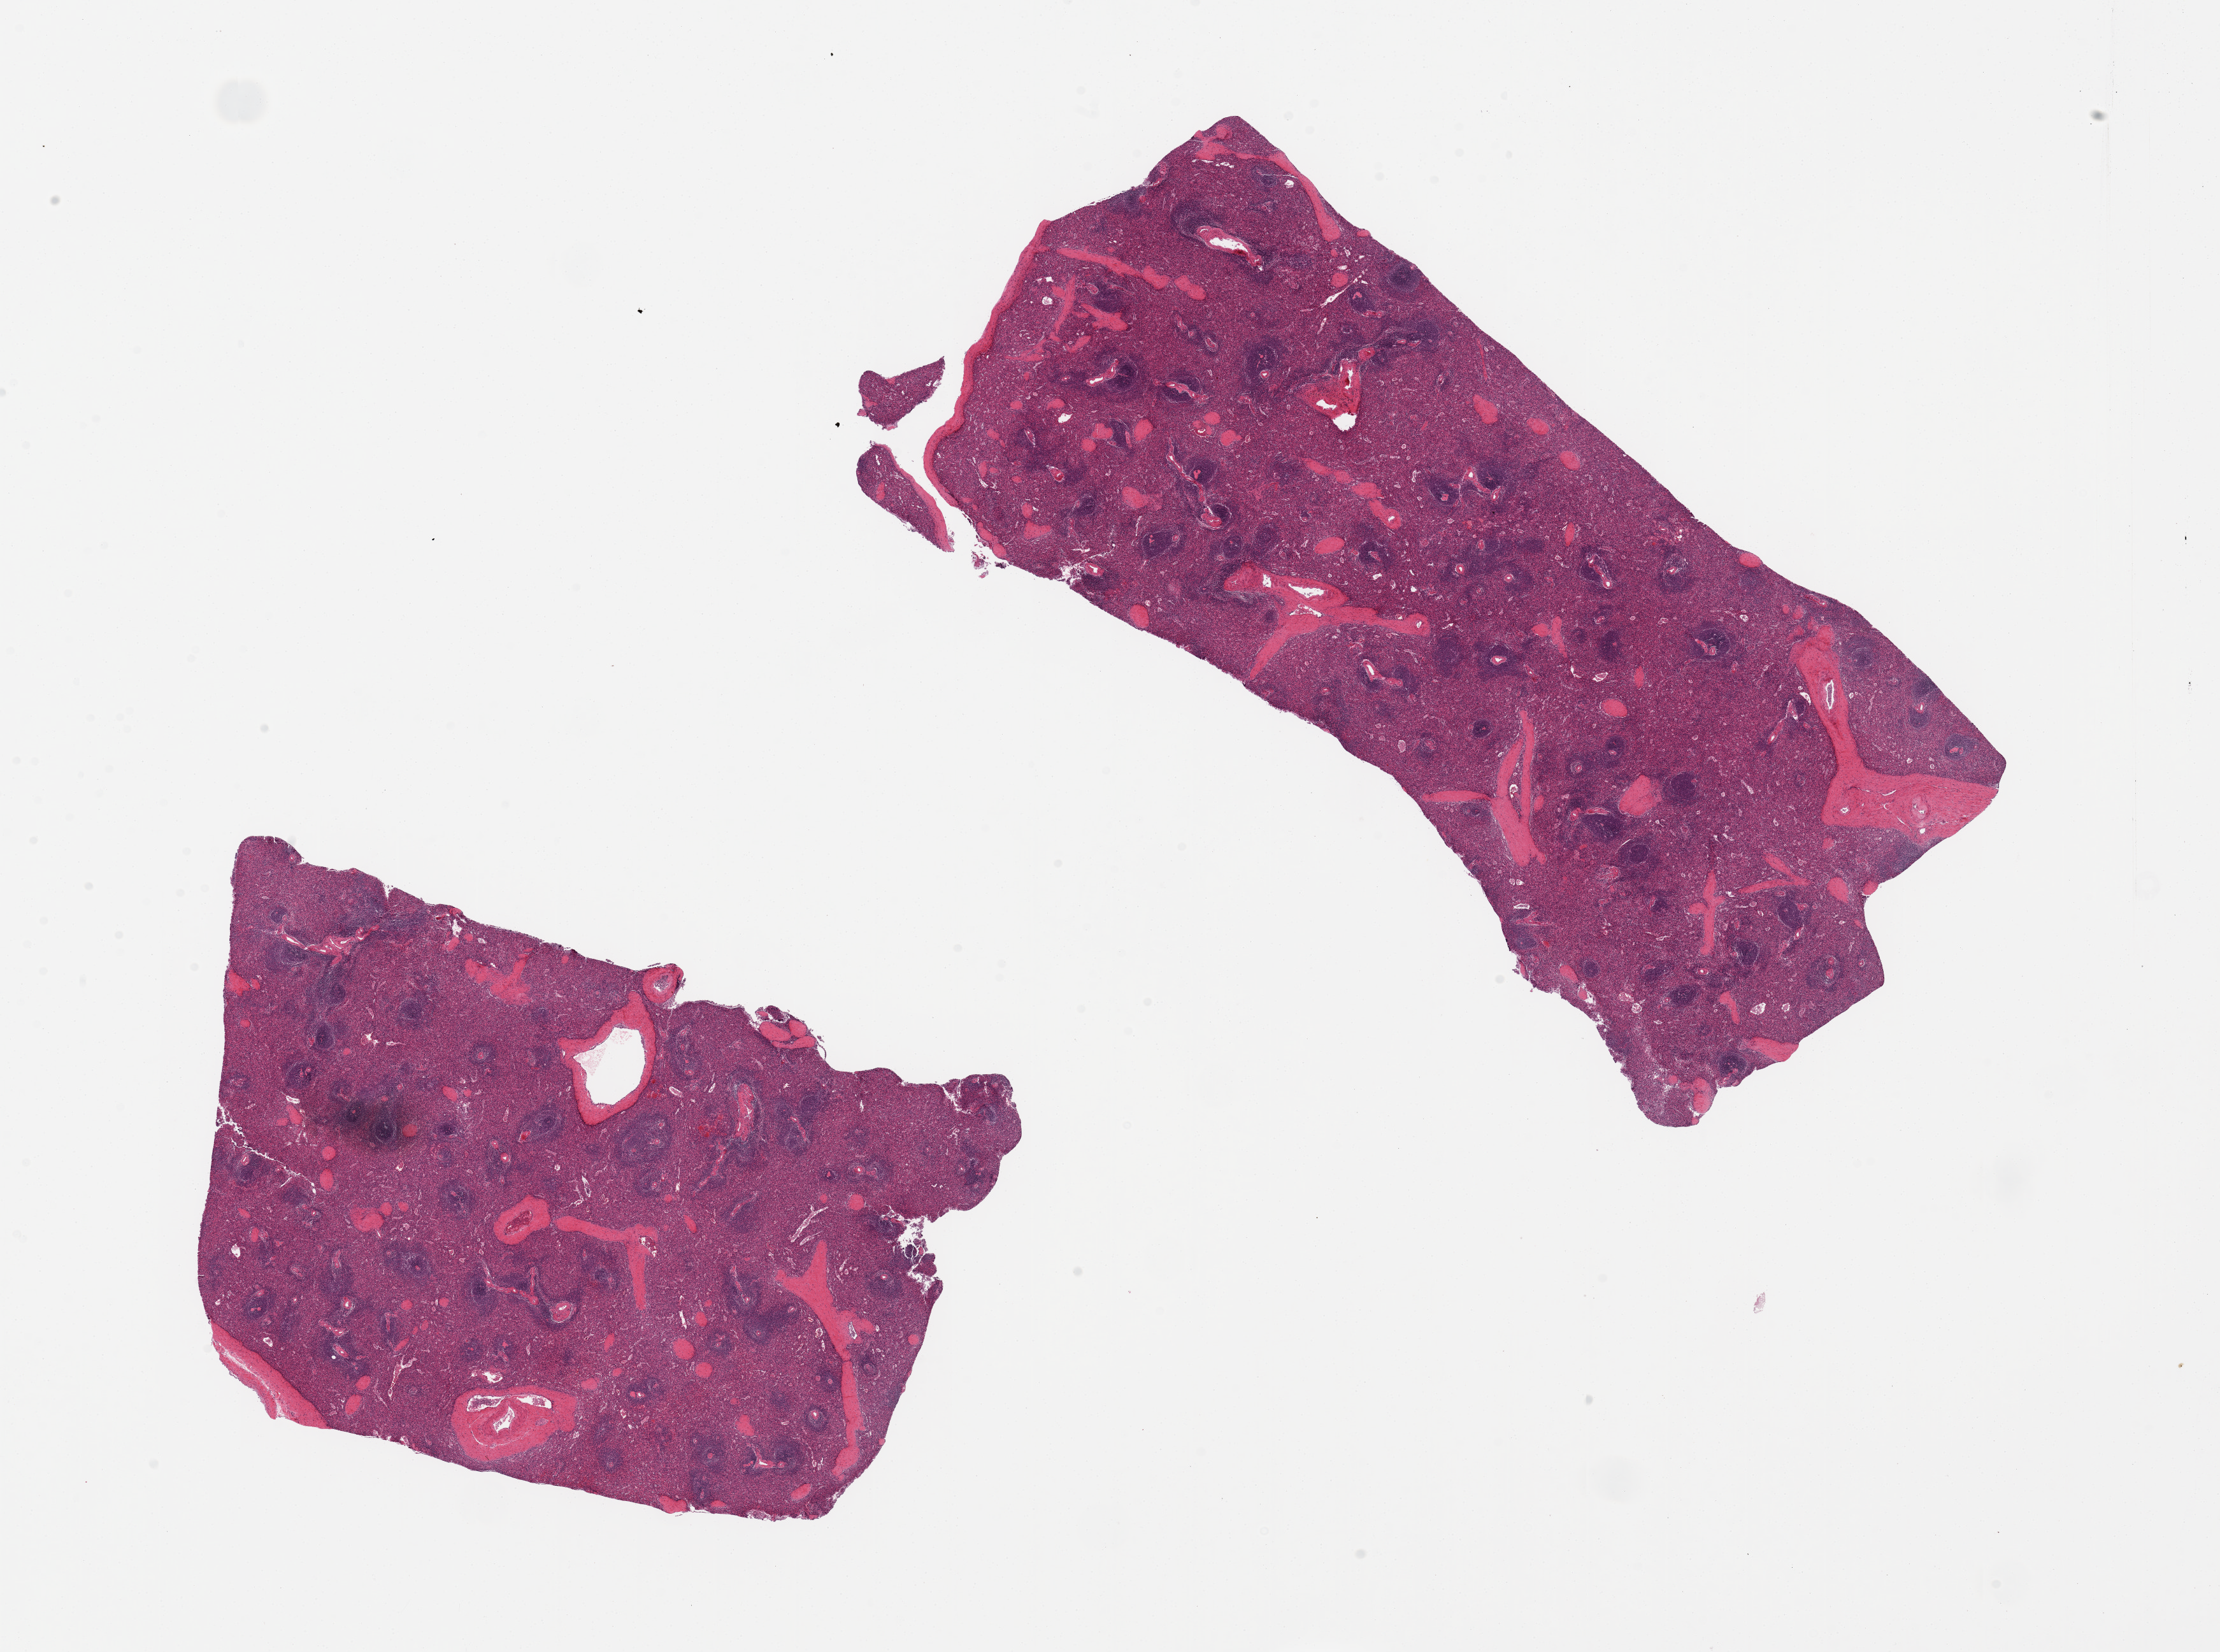
H&E whole-slide image — shown as a low-resolution overview of the whole scanned area (about 27.6 x 20.5 mm, slide scanned at 20x). PAXgene-fixed, paraffin-embedded tissue. Sampled site (target tissue): spleen. Tissue donor sample.
Review note (as recorded): 2 pieces, 10x7 & 14x7mm; milde congestion.